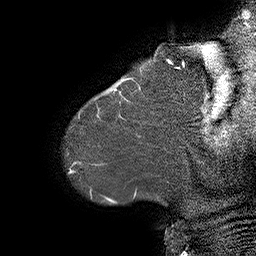
Breast MRI (dynamic contrast-enhanced), one sagittal slice. Position 2 of 55 along the scan axis. Dynamic contrast-enhanced series, time point 2 of 6 at this slice position (early post-contrast). 1.5 T. TE 4.5 ms, TR 32.4 ms. 256 × 256 image matrix, field of view 180 × 180 mm. Female patient. From the clinical record (not read from this slice): setting: breast cancer imaged before/during neoadjuvant chemotherapy; receptor status: HER2-positive.
Annotated regions visible in this slice (semi-automatically segmented with operator editing):
- analysis volume of interest (the breast-tissue region the enhancement analysis was run in; not a lesion): bounding box (x1, y1, x2, y2) in pixels: (80, 64, 163, 134)
- tumour enhancement mask (voxels above the 100 % enhancement threshold inside the analysis volume of interest): (114, 79, 128, 93)